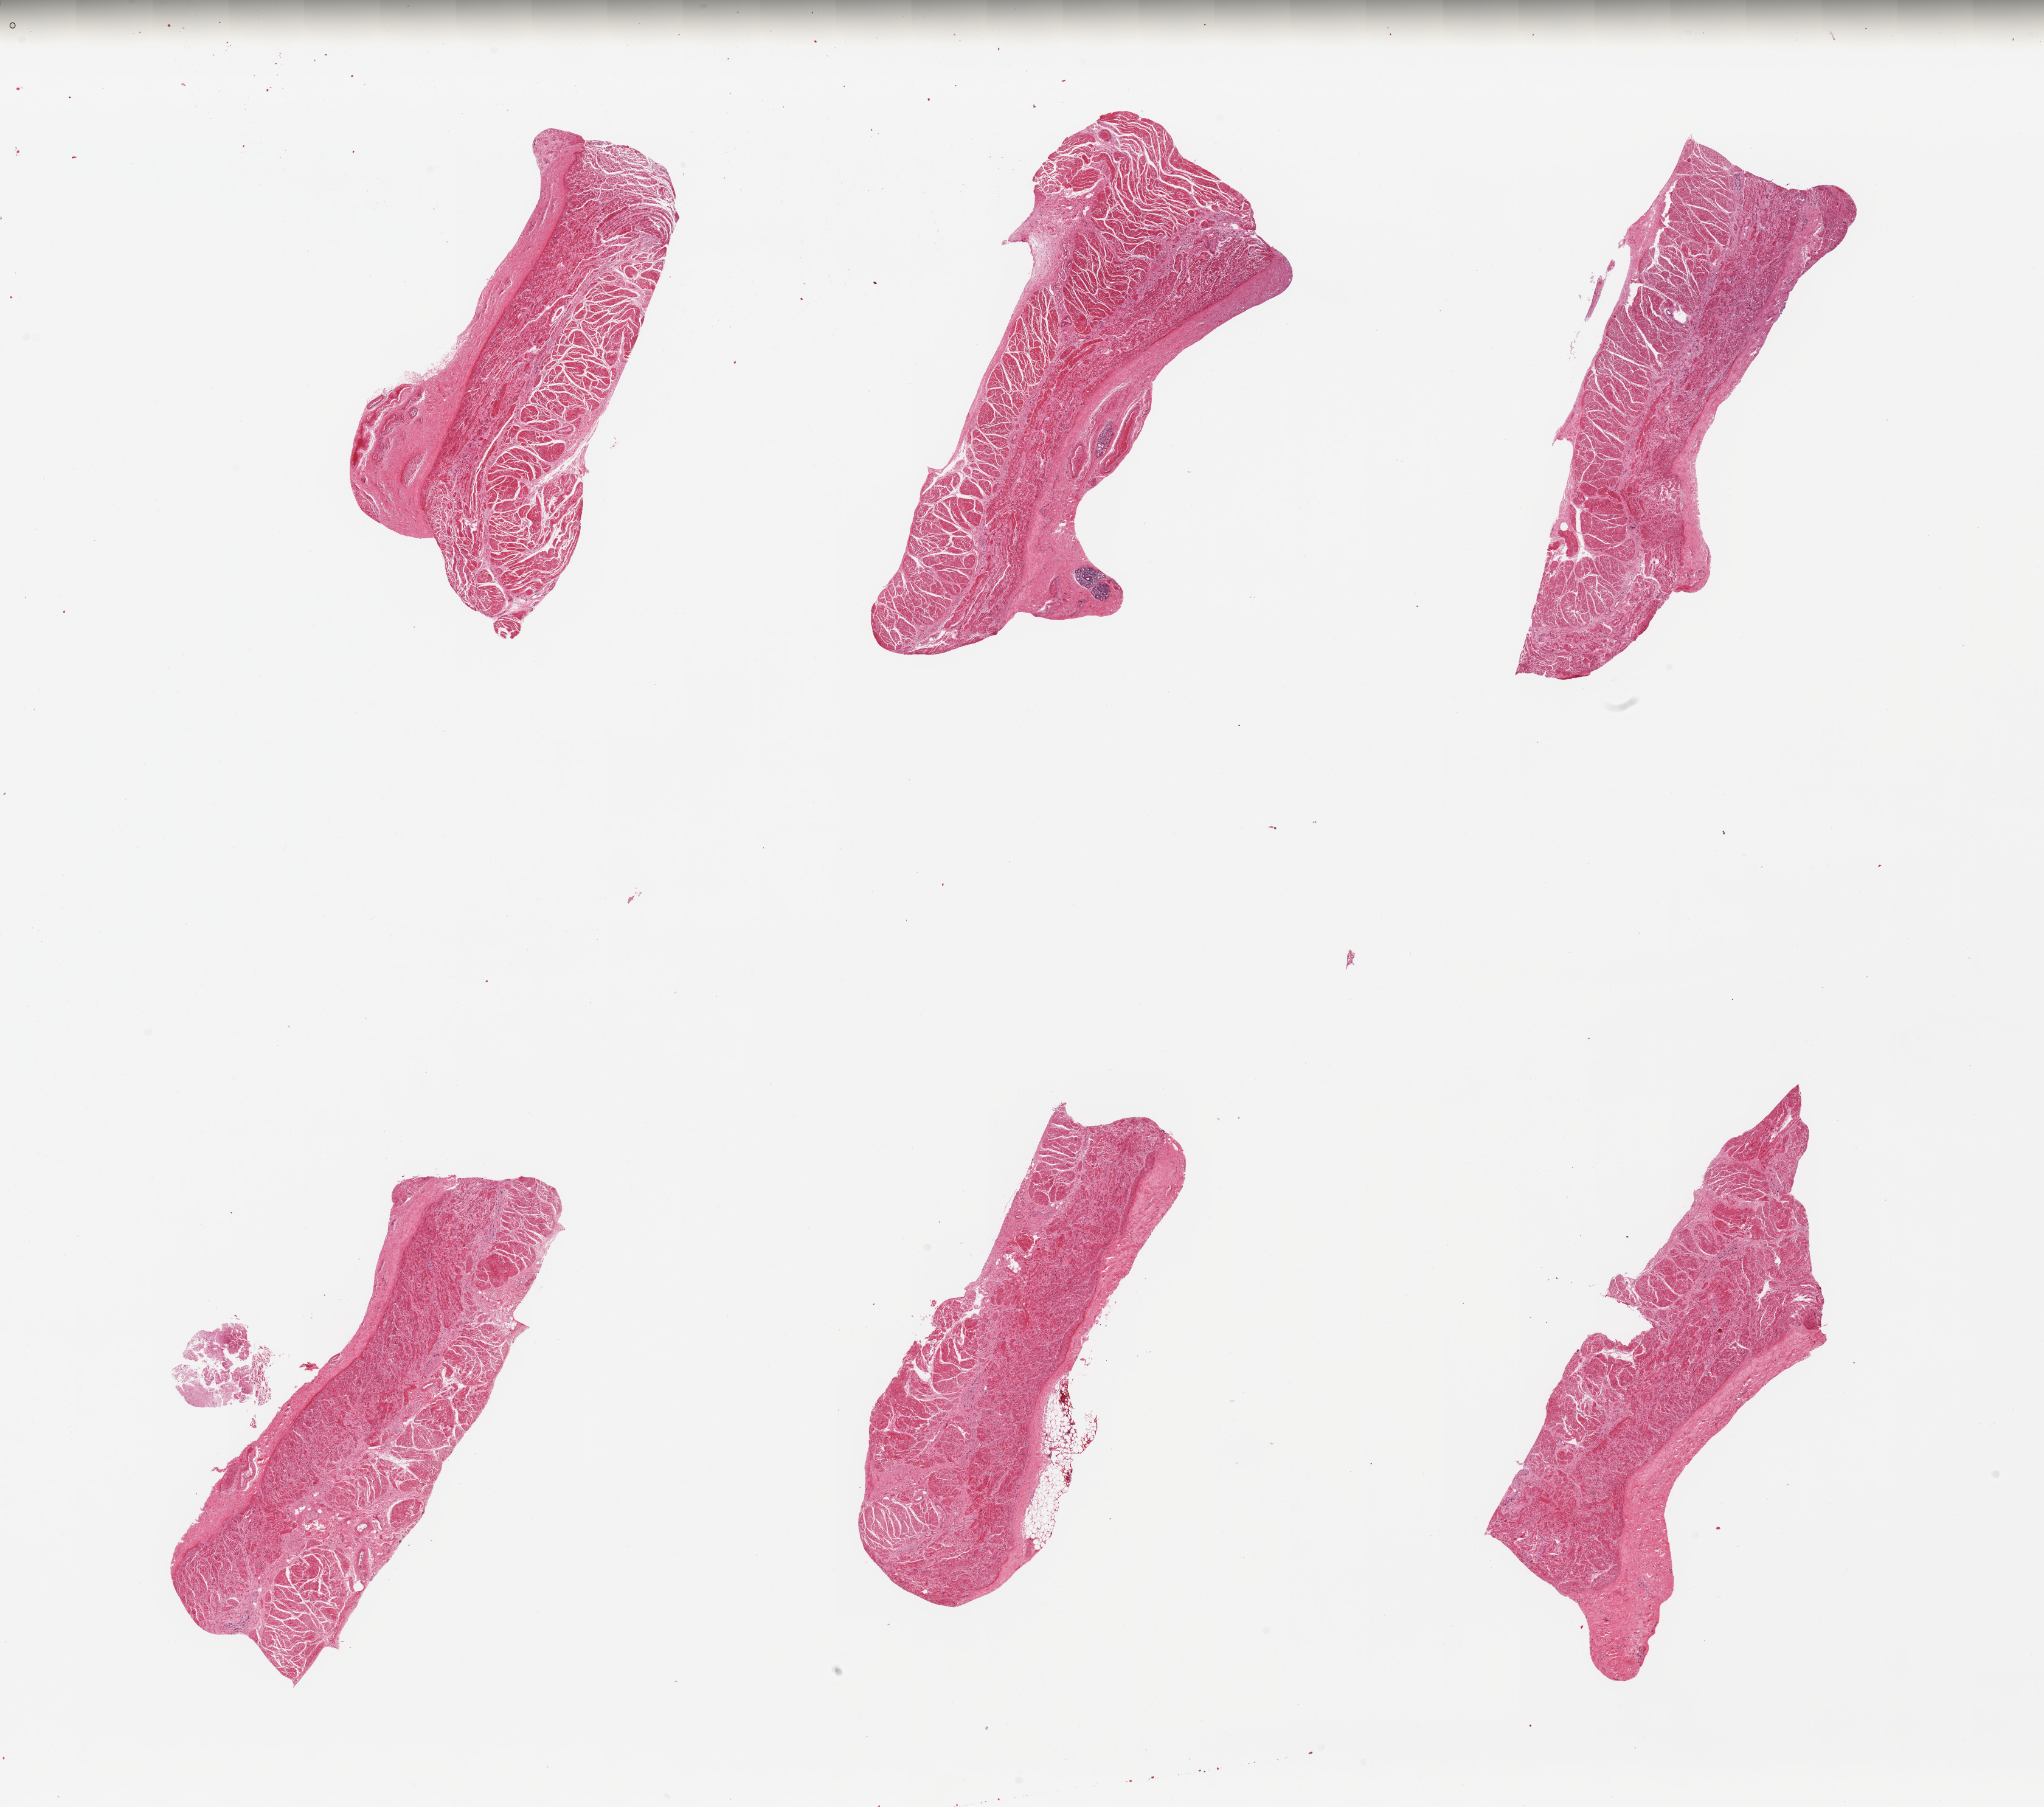
Whole-slide image, hematoxylin and eosin (H&E) stain, brightfield — a low-resolution overview of the entire scanned area, about 26.6 x 23.5 mm. PAXgene-fixed paraffin-embedded (PFPE) section. Section of esophageal muscle (target tissue). Donor tissue sample. Donor sex: female.
Reviewer comment on this tissue sample: 6 pieces, confirmed target muscularis.